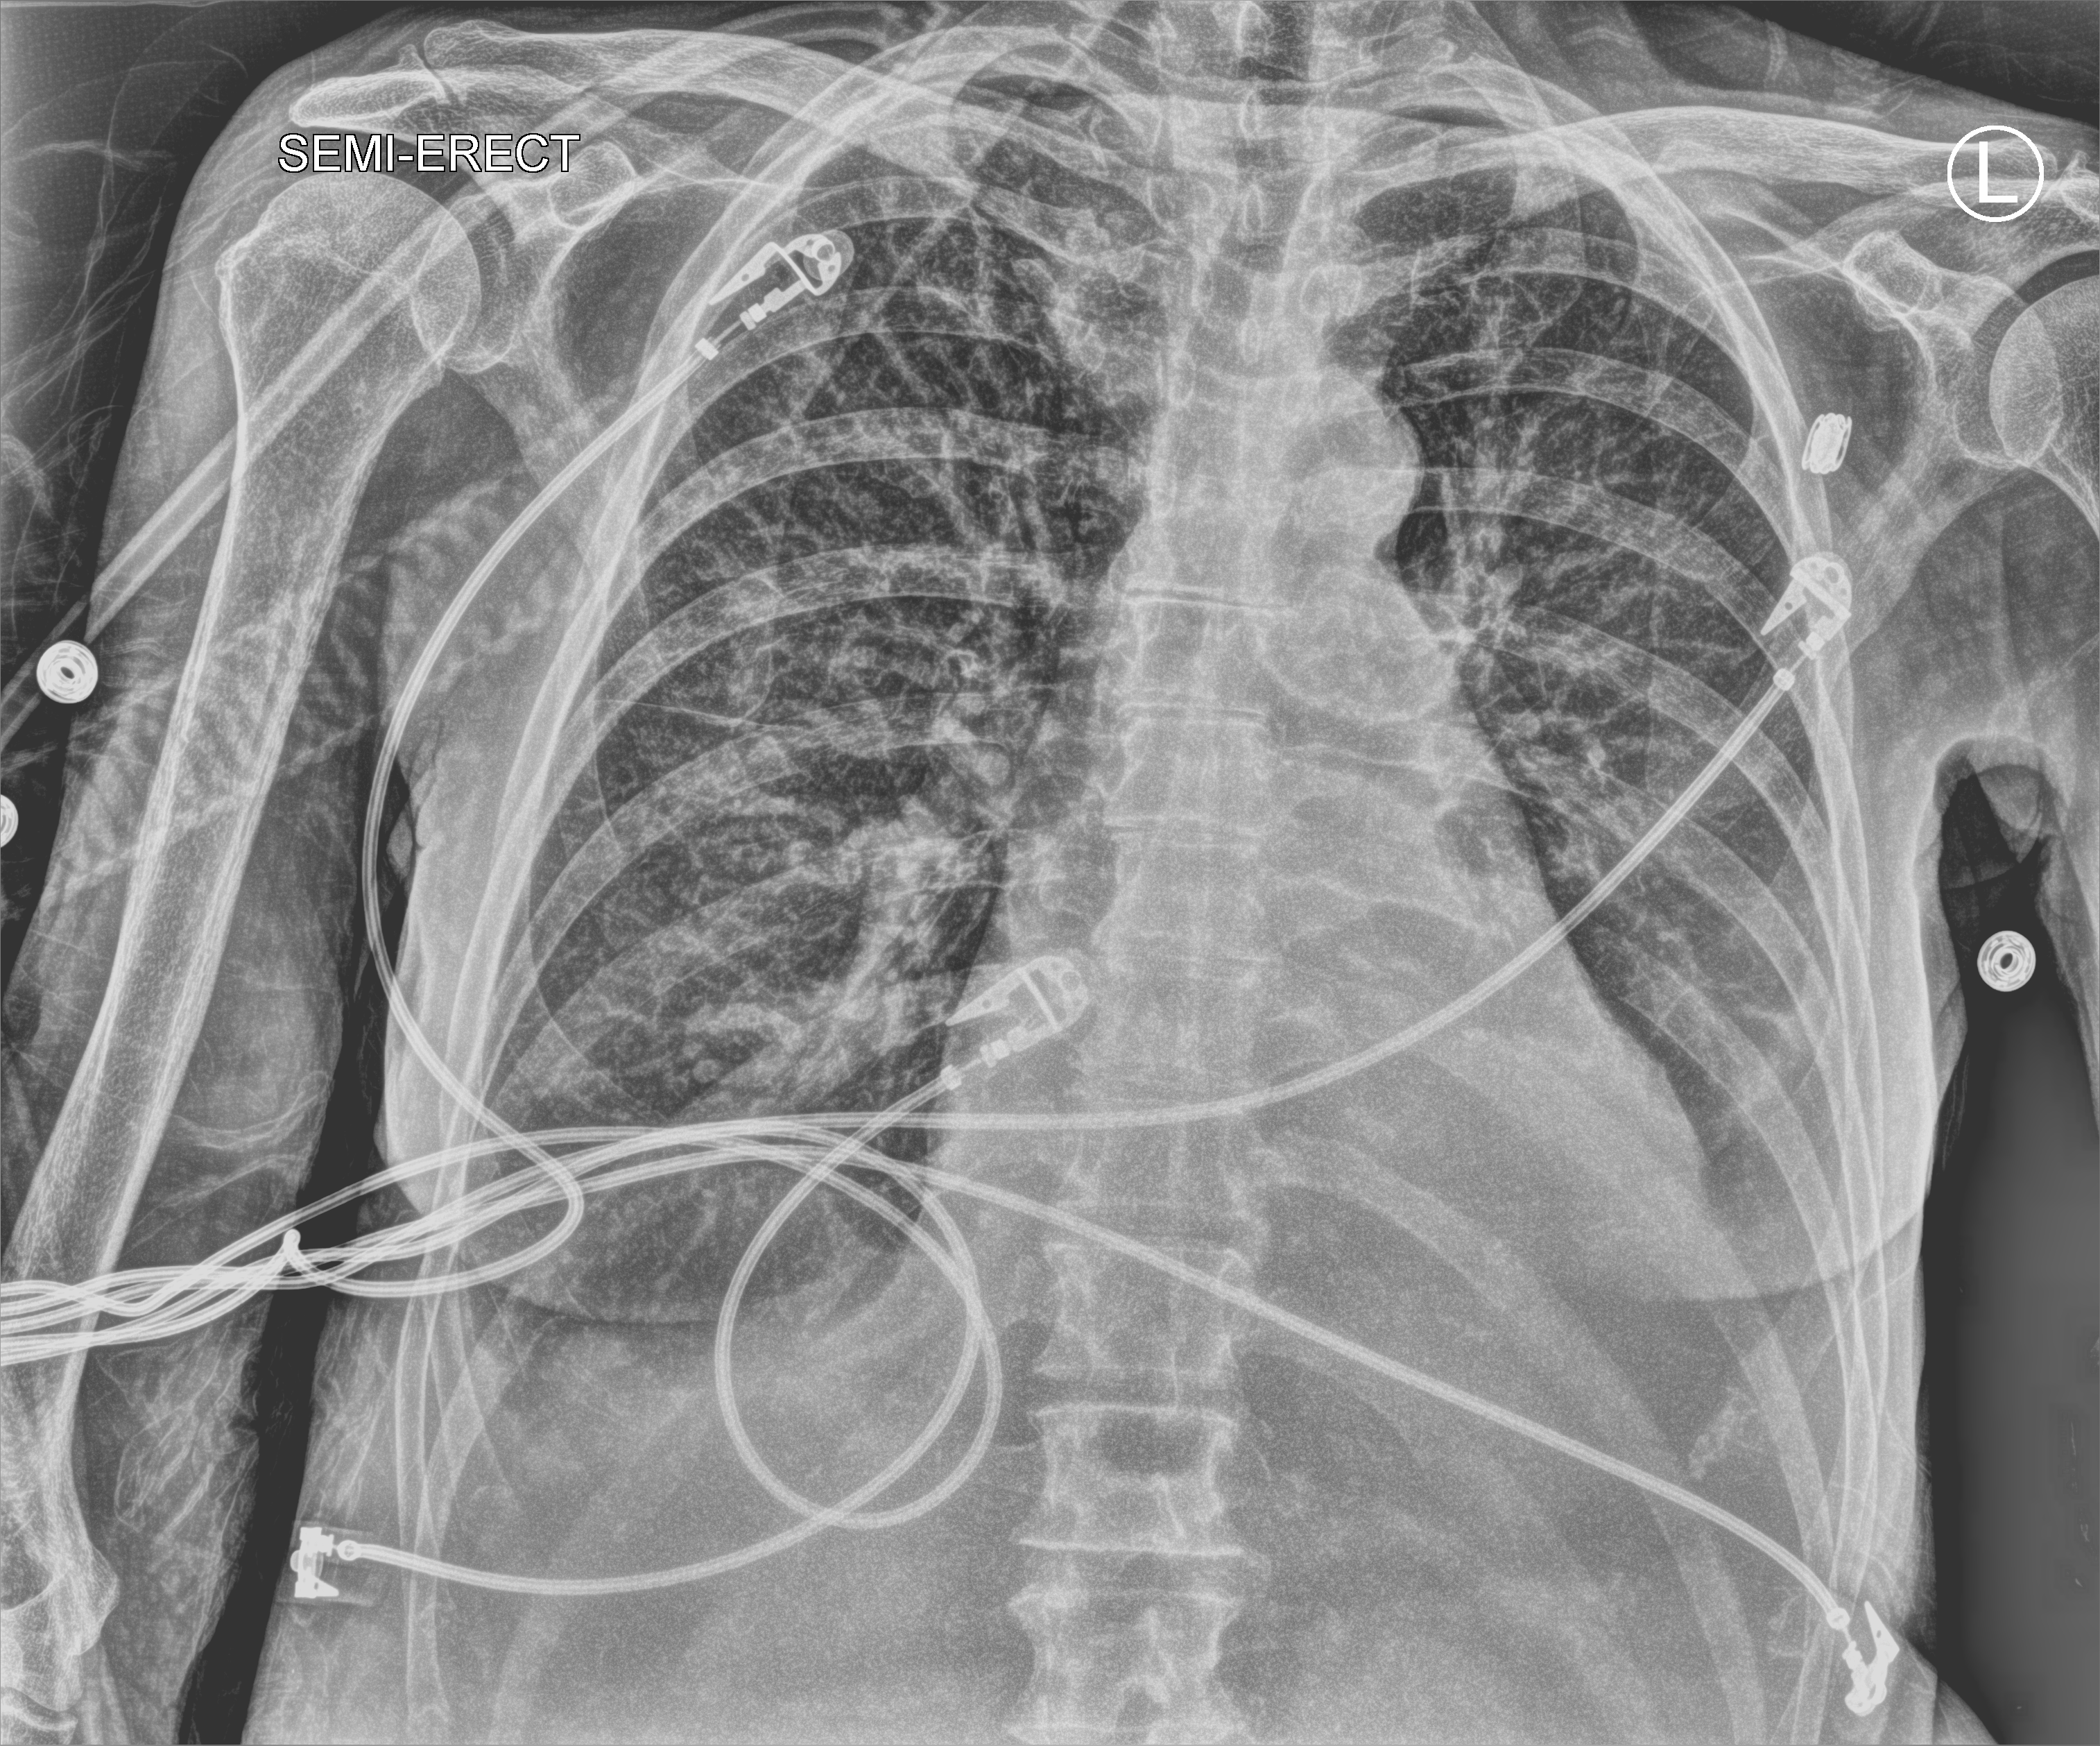
Portable chest radiograph; anteroposterior (AP) projection. Female patient hospitalised with COVID-19, age 60–74 years.
Admission-level facts for this patient (not findings on this image; timing relative to this image not recorded): mechanically ventilated during this hospital stay: yes; length of hospital stay: 38 days.